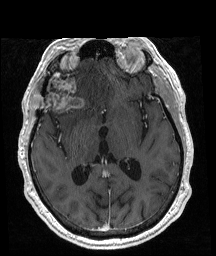
Brain MRI from a brain-tumour surgery series, one axial slice; position 100 of 192 along the scan axis; T1-weighted post-contrast; 1 mm slice thickness; 216 × 256 image matrix. Case-level facts recorded for this patient, not image findings: histopathology: Glioblastoma; WHO grade: 4; IDH mutation: no; tumour location: Right Frontal.
Structures marked on this image (expert manual segmentation):
- previous resection cavity: bounding box (x1, y1, x2, y2) in pixels: (51, 86, 54, 91)